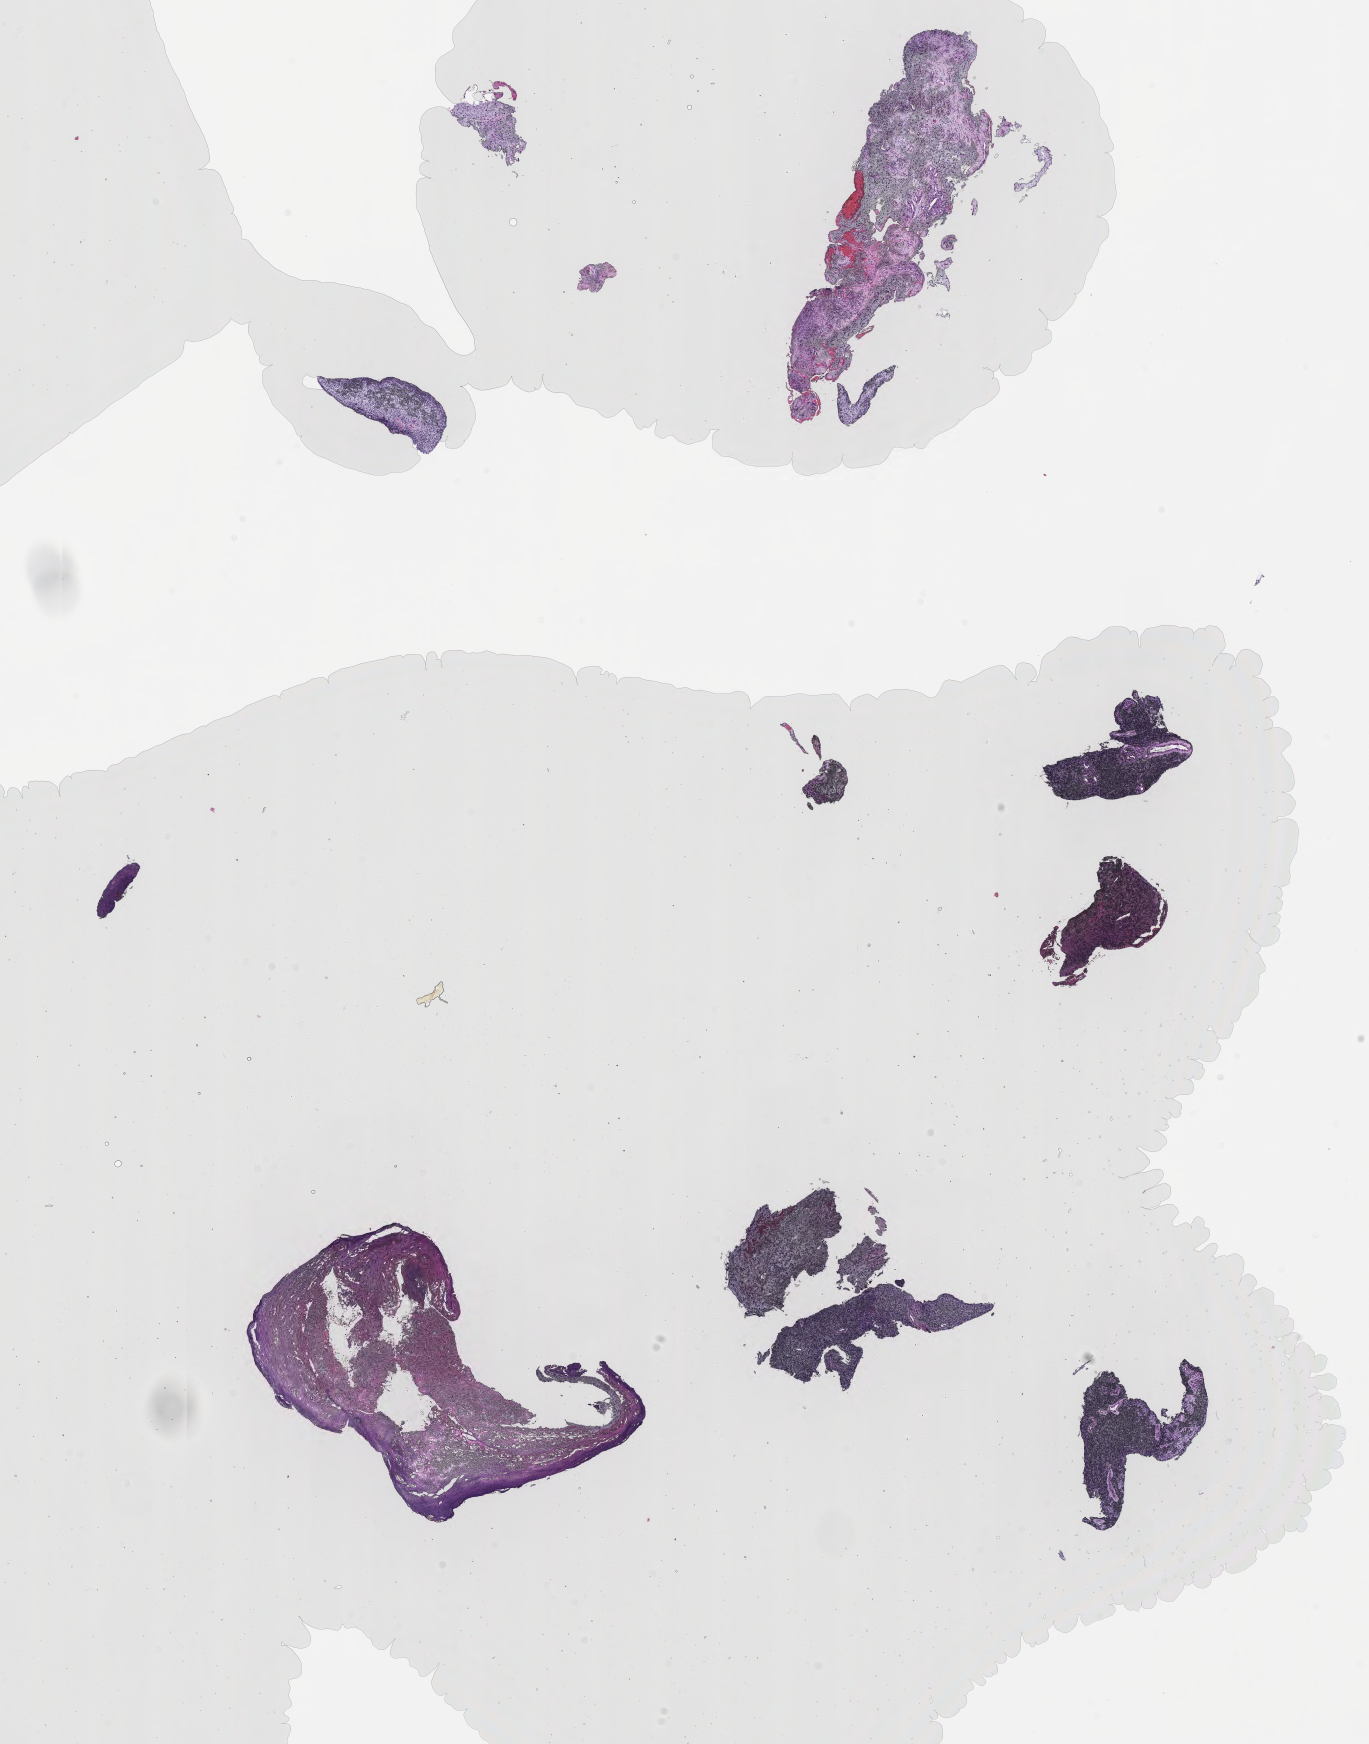
H&E whole-slide image of tumor tissue from the external ear, a low-resolution overview of the entire scanned area, about 11.1 x 14.1 mm, FFPE section. Patient male; age 61 months (5 years 1 month).
• diagnosis: Rhabdomyosarcoma, NOS